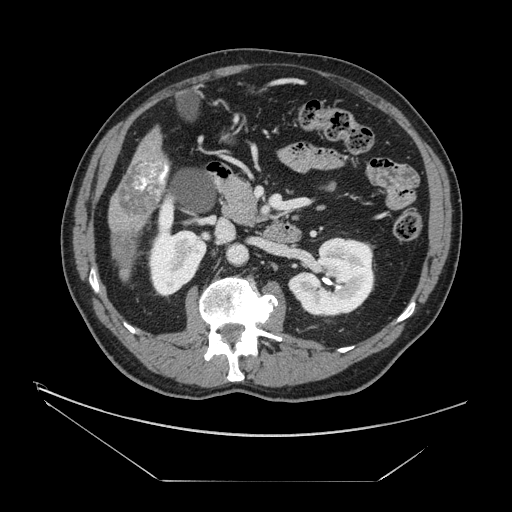
Contrast-enhanced abdominal CT, one axial slice. Position 59 of 161 along the scan axis. Intravenous contrast given. Soft-tissue window (W 400 / L 40 HU). 512 × 512 image matrix. Male patient, age 65 years. From the clinical record (not read from this slice): diagnosis: colorectal cancer liver metastases, imaged before liver resection; multiple liver metastases: yes; largest metastasis: 4.2 cm.
Annotated regions visible in this slice (manually delineated by an expert):
- liver: bounding box (x1, y1, x2, y2) in pixels: (110, 131, 169, 278)
- portal vein (with intrahepatic branches): (136, 164, 168, 193)
- liver metastasis: (114, 230, 136, 269)
- liver metastasis: (118, 160, 169, 218)